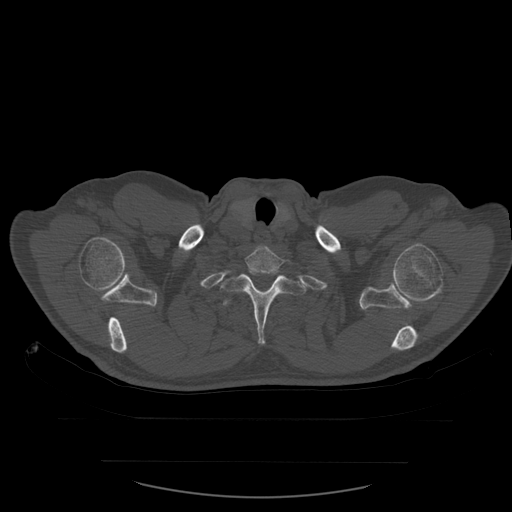
CT including the spine, one axial slice. Slice 478 of 590 in the series (ordered by position). Bone window (W 1800 / L 400 HU). 512 × 512 image matrix. Patient age 71 years. Case-level facts recorded for this patient, not image findings: primary cancer: lung.
Structures marked on this image (semi-automatically segmented with operator editing):
- T1 vertebra: box from (x=246, y=246) to (x=285, y=277) px
- T2 vertebra: (x=220, y=270)–(x=313, y=345)
- T3 vertebra: (x=223, y=299)–(x=234, y=307)